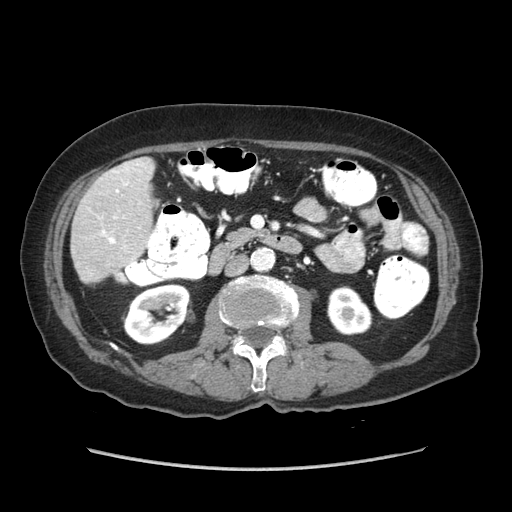
Contrast-enhanced abdominal CT (liver protocol), one axial slice; slice 19 of 89 in the series (ordered by position); reconstruction kernel STANDARD; 140 kVp; soft-tissue window (W 400 / L 40 HU); 2.5 mm slice thickness; 512 × 512 image matrix, field of view 360 × 360 mm. Case-level facts recorded for this patient, not image findings: diagnosis: hepatocellular carcinoma (patient treated with transarterial chemoembolisation; whether this scan precedes or follows treatment is not stated here); TNM stage (as recorded): Stage-IIIA; Child-Pugh class: A.
Outlined on this slice (semi-automatic segmentation, software-assisted and operator-edited):
- liver parenchyma outside the tumour (the mass and vessels are separate outlines, so this box may not span the whole liver): bounding box <70,158,154,282> (left, top, right, bottom; pixels)
- liver vessels: <101,164,138,244>